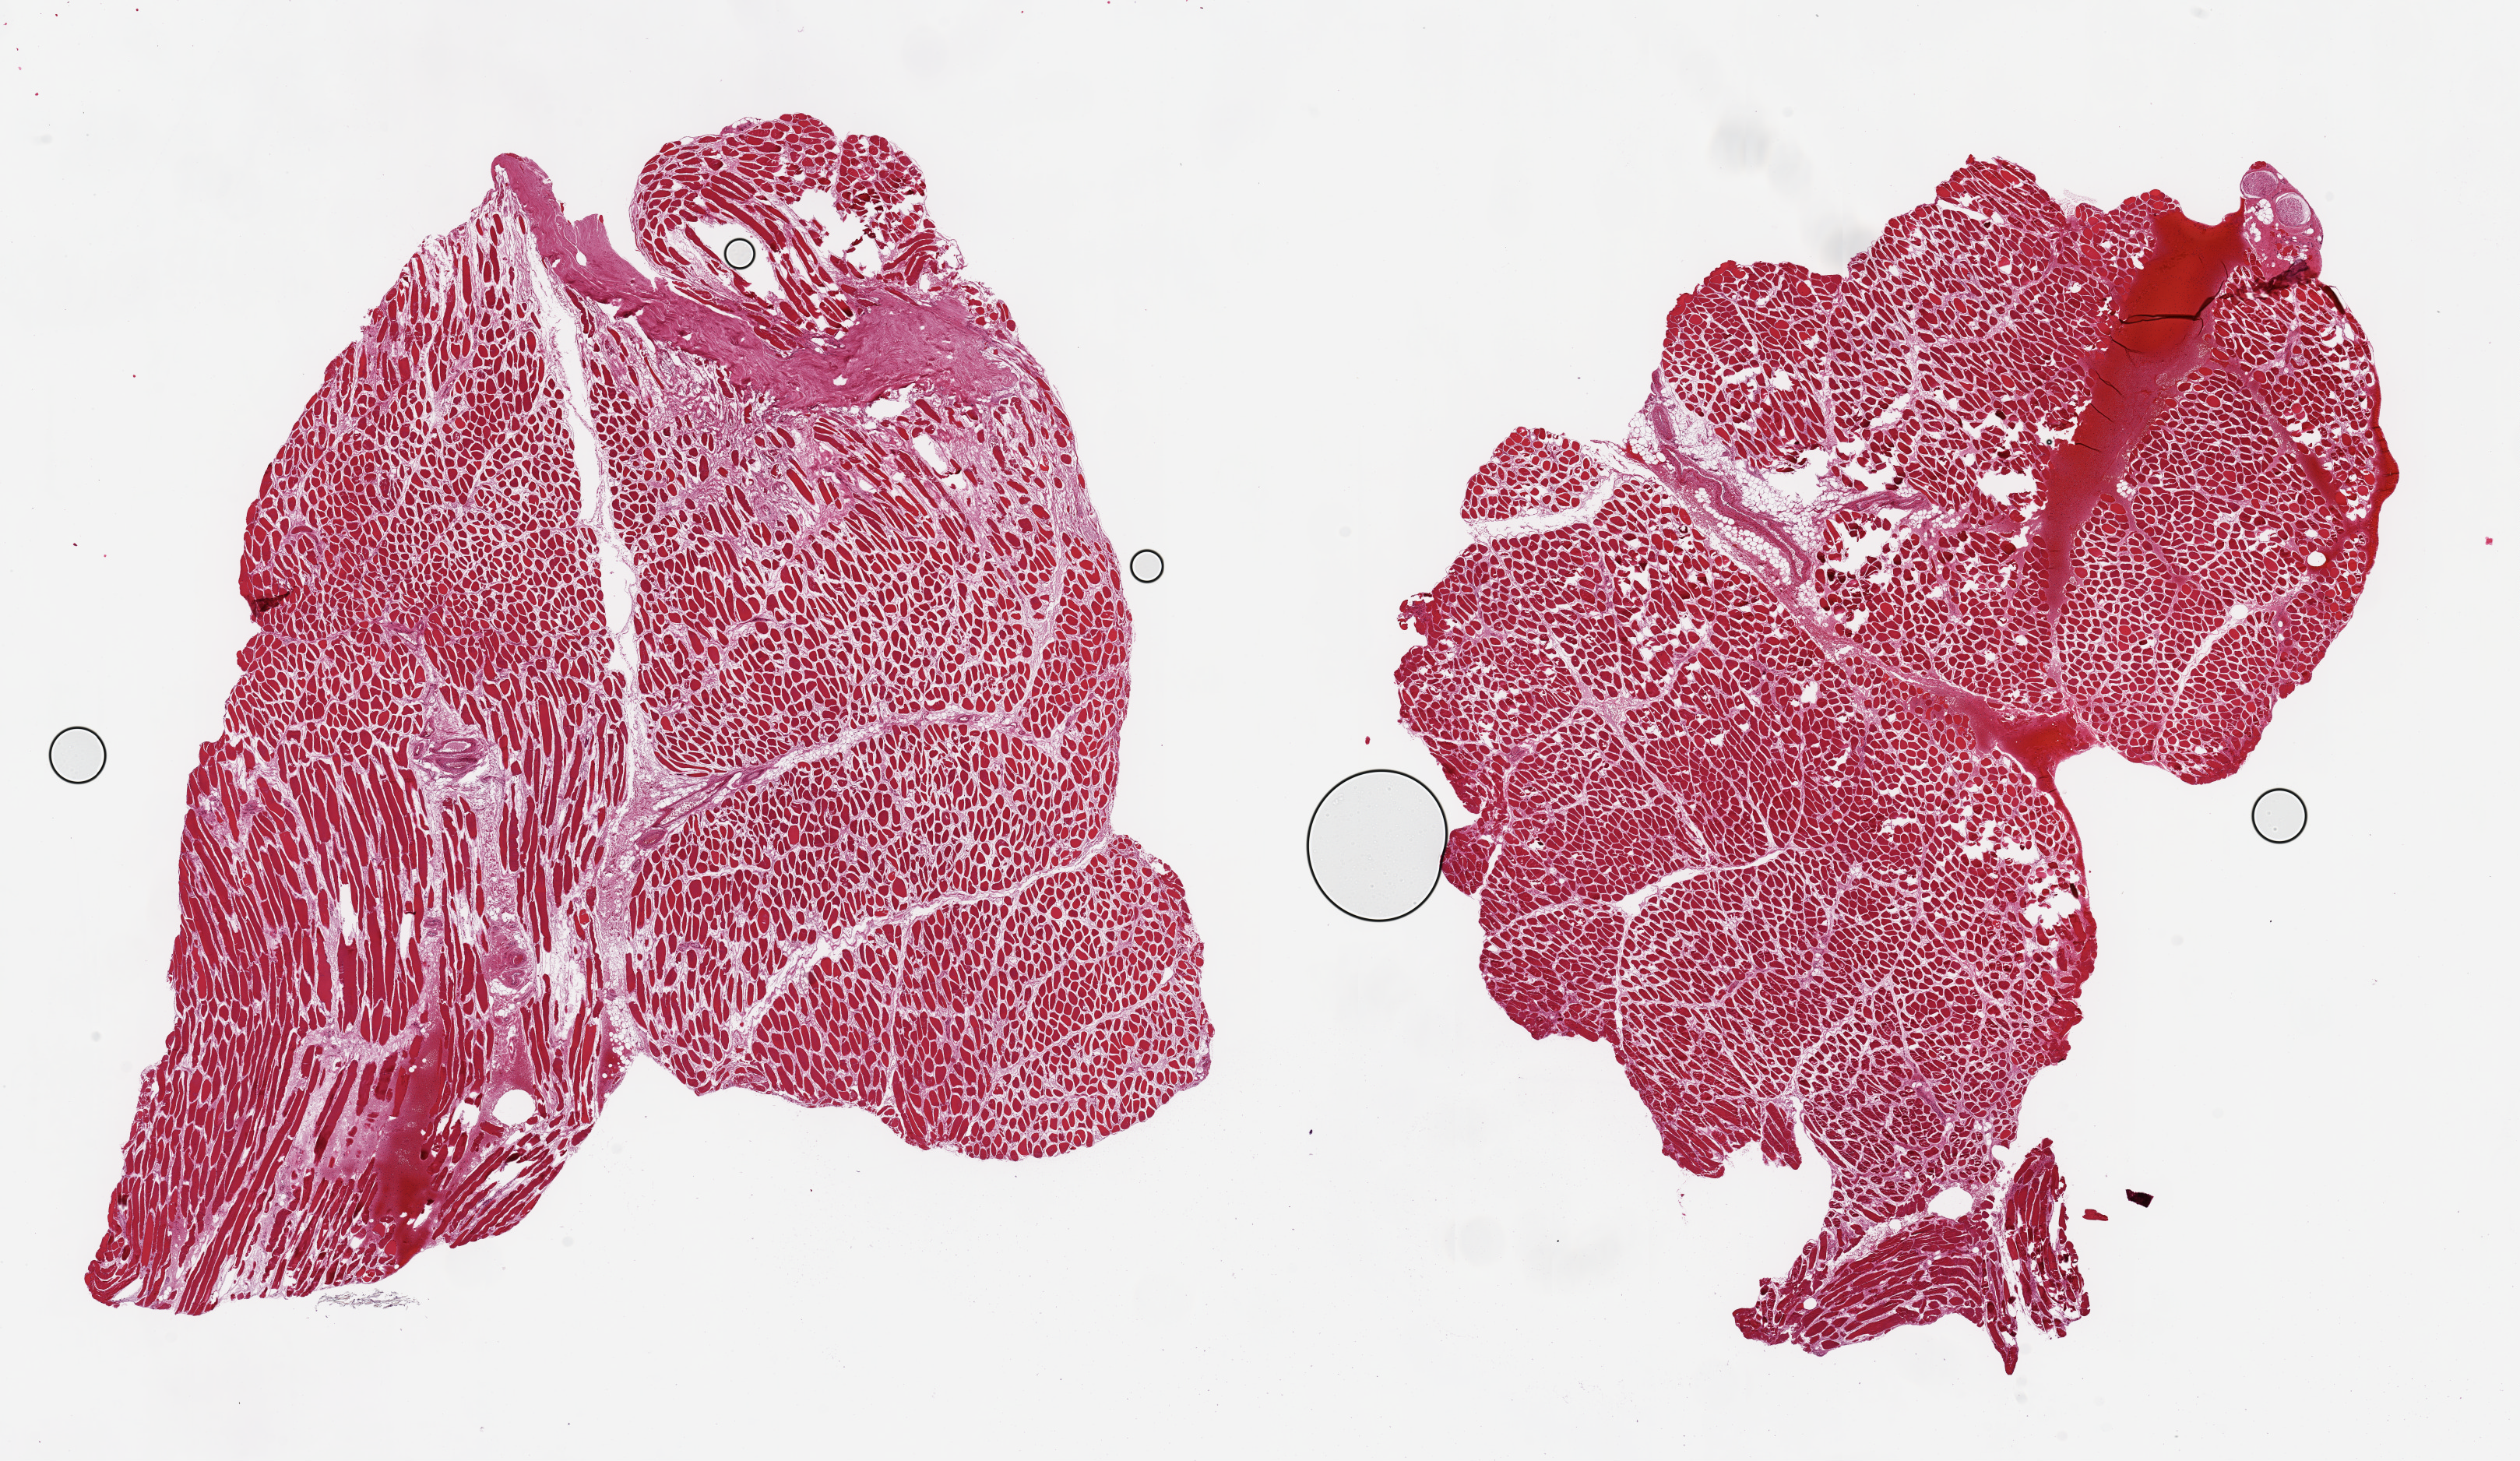
Digitized haematoxylin and eosin-stained section, brightfield, whole scanned area (about 25.6 x 14.8 mm) shown as a low-resolution overview, PAXgene-fixed, paraffin-embedded tissue, sampled site (target tissue): skeletal muscle, donor tissue sample. Donor sex: male.
Reviewer comment on this tissue sample: 2 pieces, 12.5x11 & 11x9mm; prominent focal hemorrhages and interstital edema; <5% adipose.